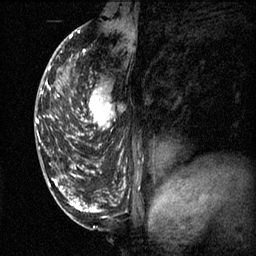
Breast MRI (dynamic contrast-enhanced), one sagittal slice. Slice 32 of 60 in the series (ordered by position). 3 images stored at this slice position (order not interpretable as contrast timing). 1.5 T. TE 4.2 ms, TR 11.1 ms. 2 mm slice thickness. 256 × 256 image matrix, field of view 180 × 180 mm. Female patient, age 50 years.
Annotated regions visible in this slice (semi-automatic segmentation, software-assisted and operator-edited):
- analysis volume of interest (the breast-tissue region the enhancement analysis was run in; not a lesion): bounding box (x1, y1, x2, y2) in pixels: (68, 68, 124, 141)
- tumour enhancement mask (voxels above the 70 % enhancement threshold inside the analysis volume of interest): (68, 86, 121, 141)